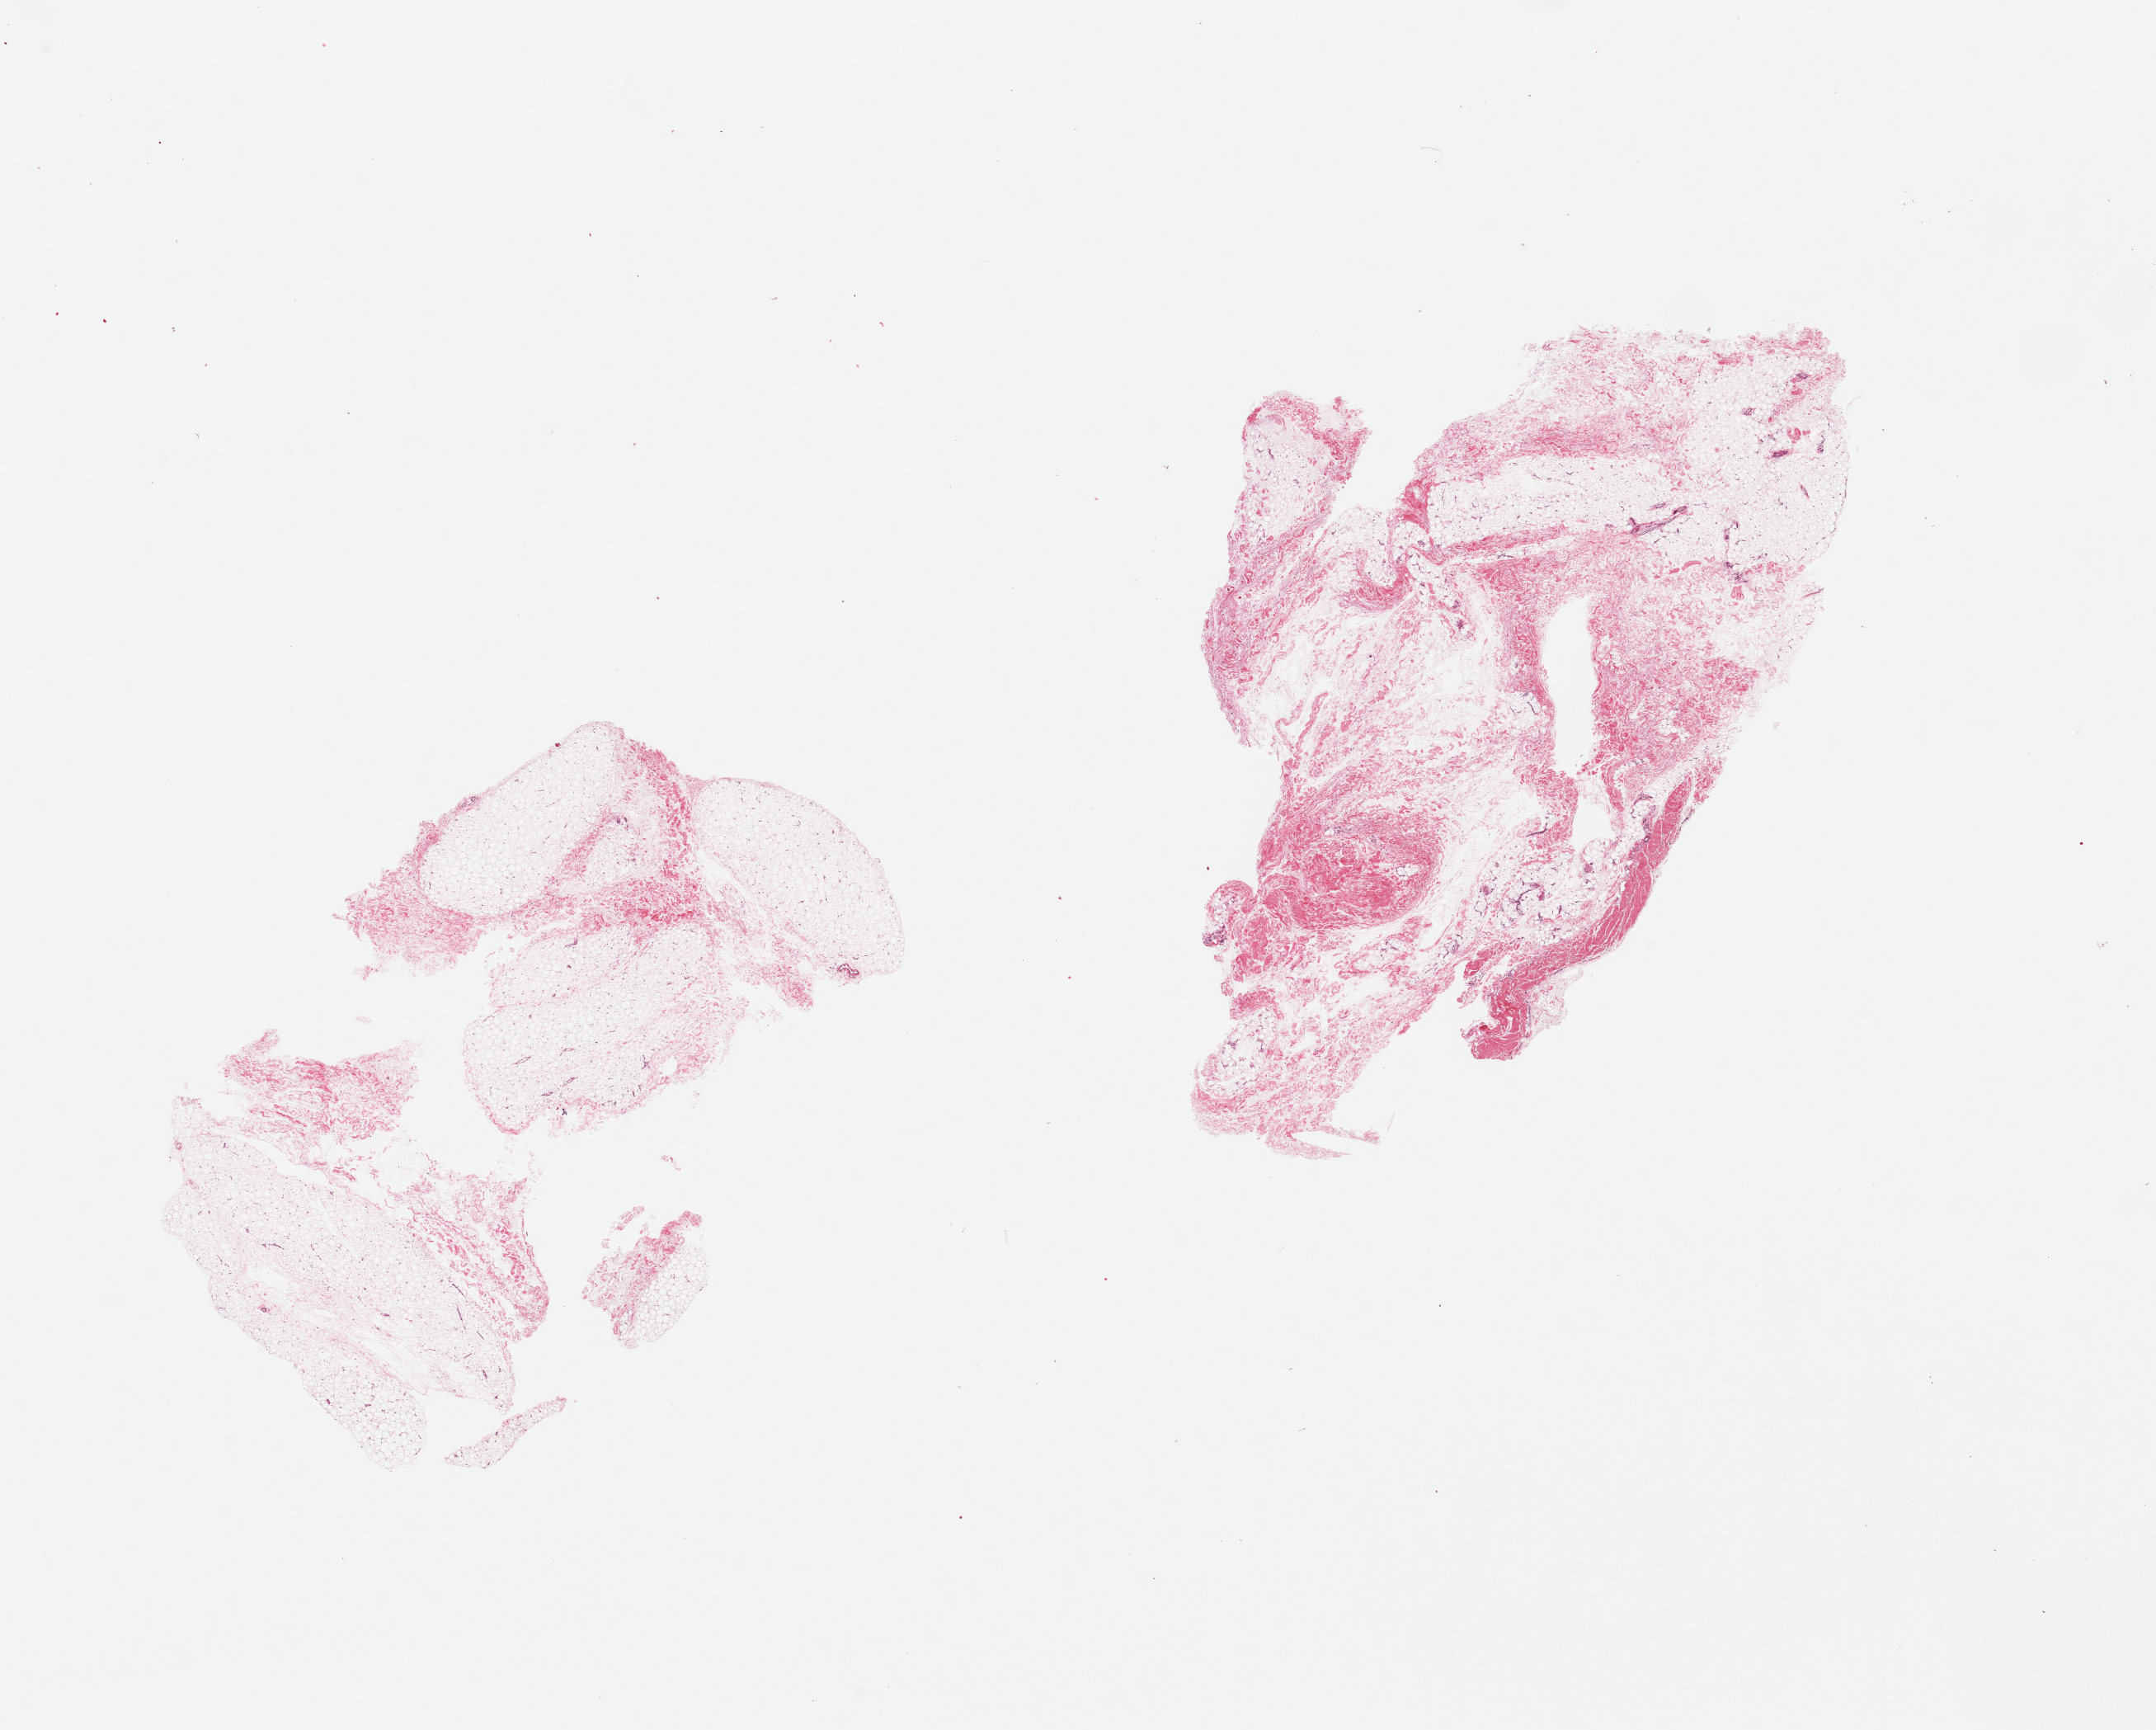
Whole-slide image, hematoxylin and eosin (H&E) stain, brightfield, a low-resolution overview of the entire scanned area, about 20.7 x 16.6 mm; PAXgene-fixed, paraffin-embedded tissue; section of adipose tissue (target tissue); donor tissue sample. Donor: male.
* reviewer comment on this tissue sample: 2 pieces, ~30% fibrous/fascial tissue